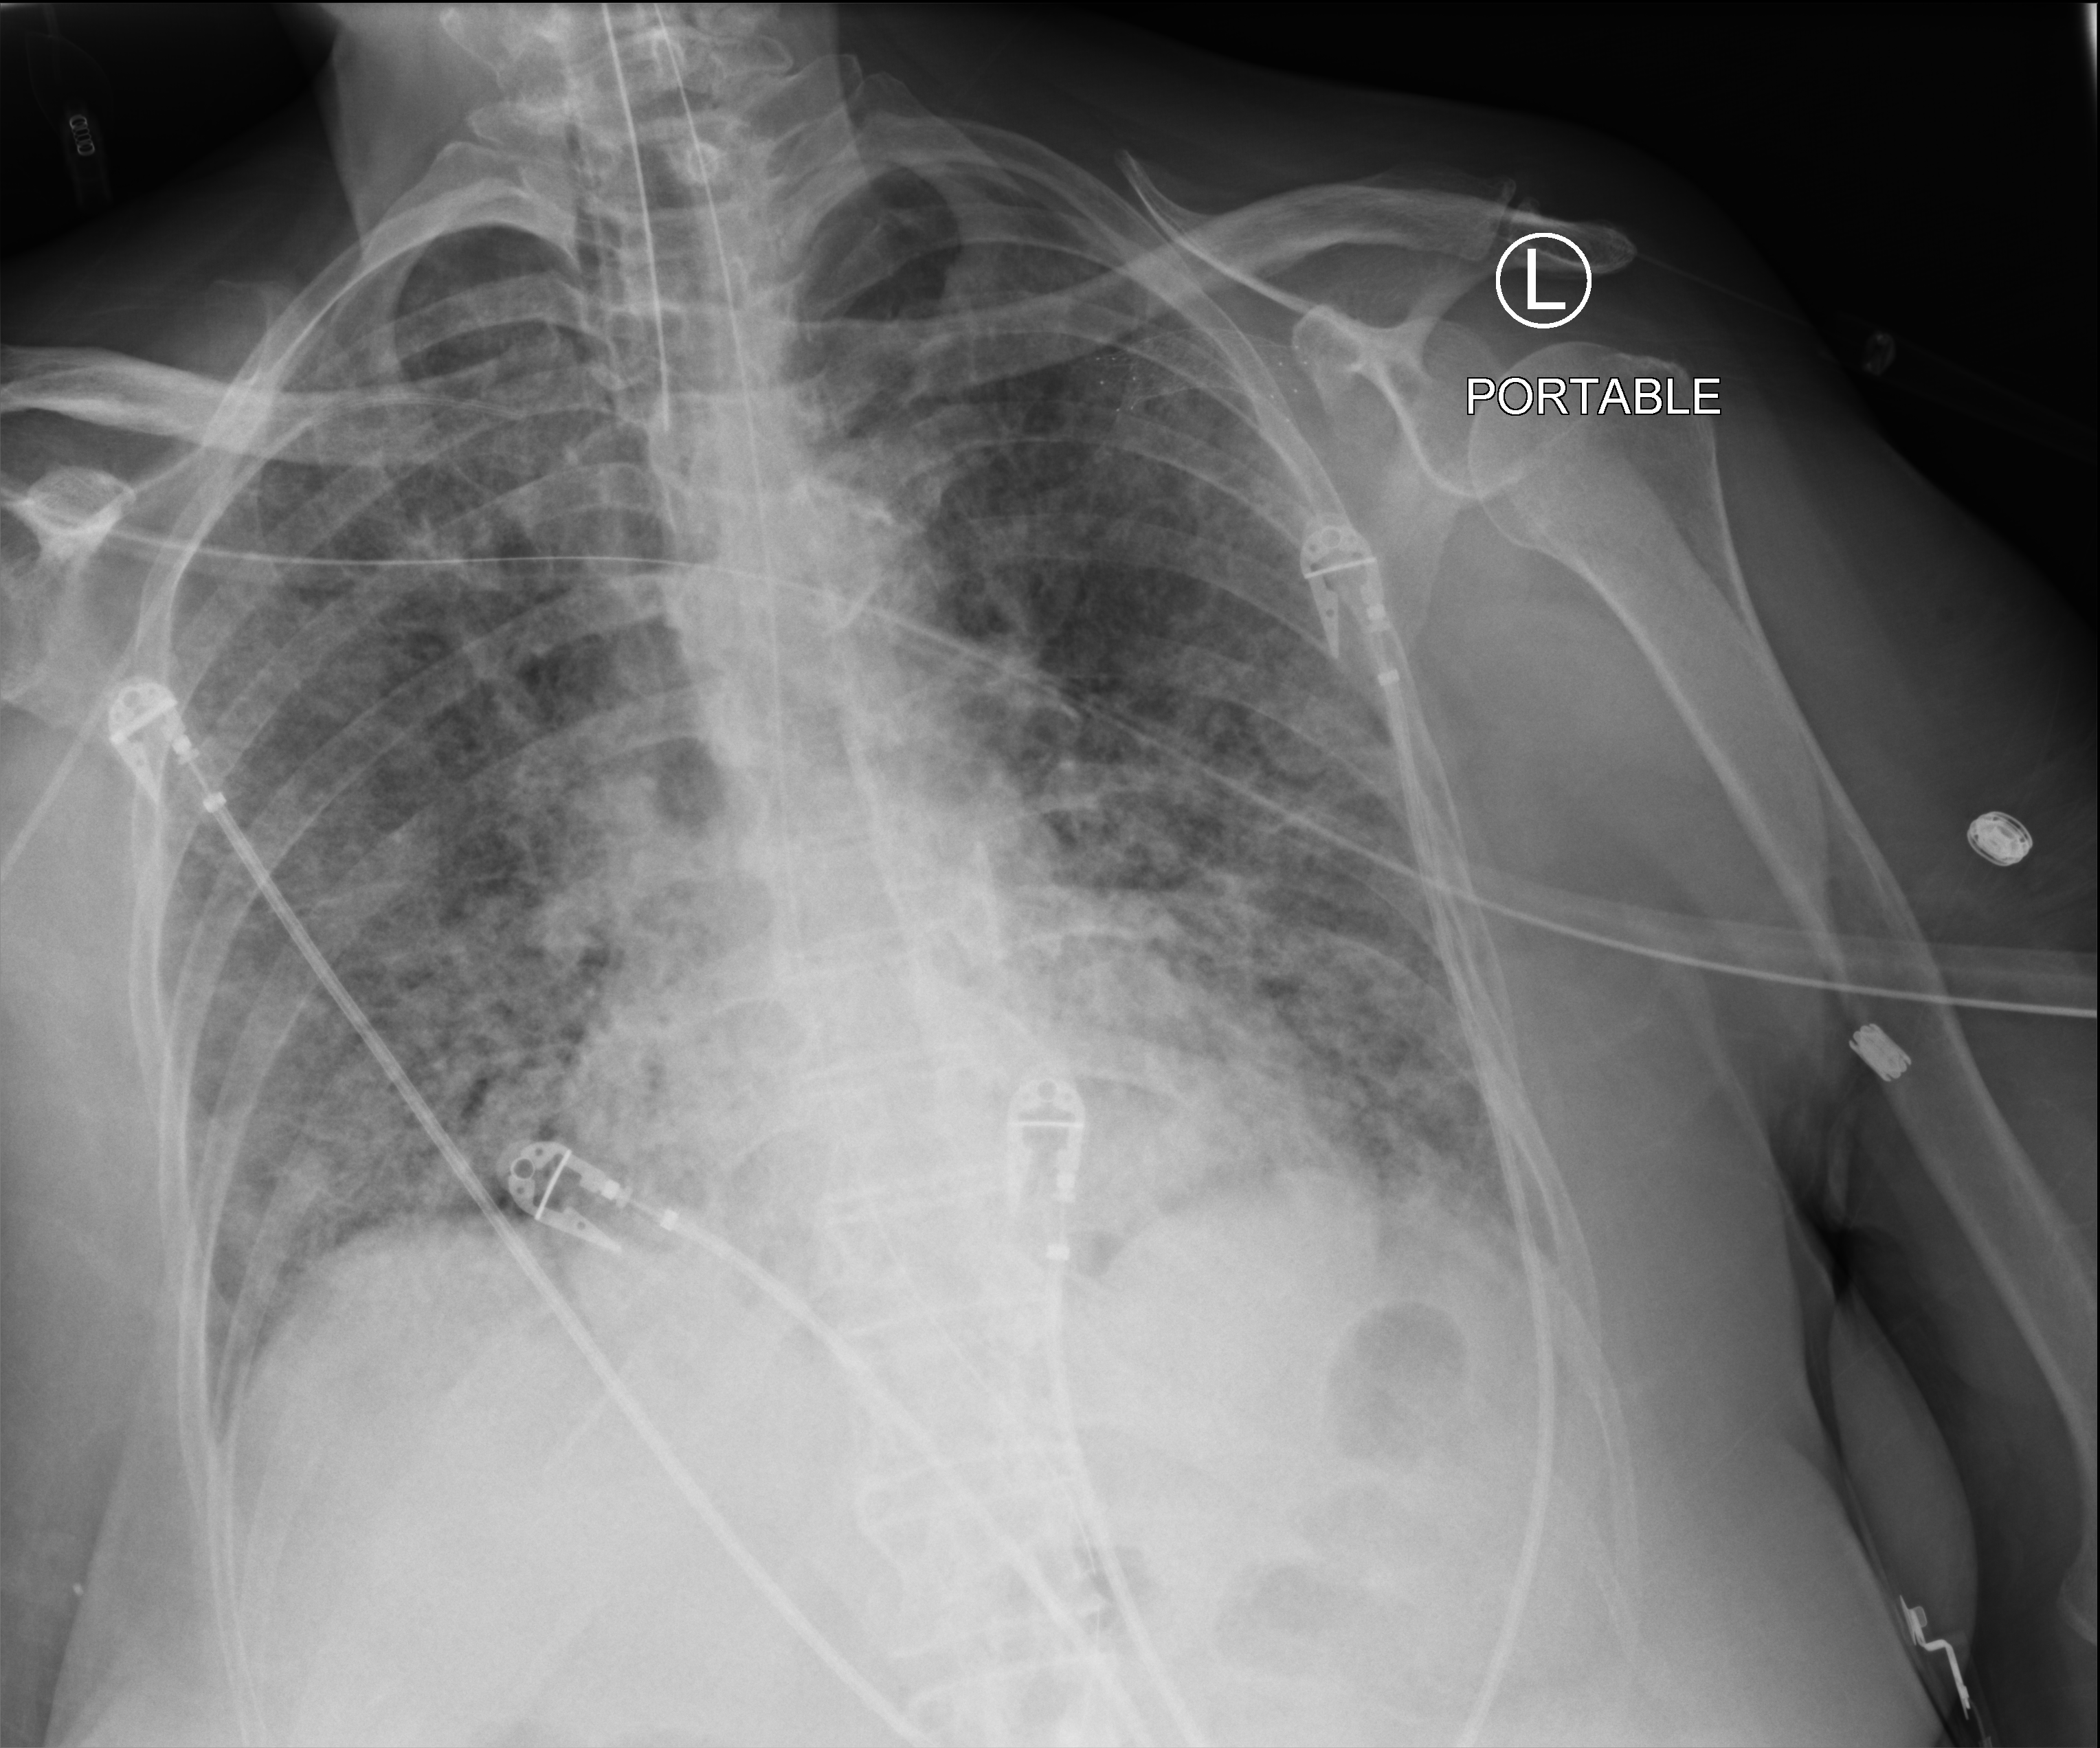
Bedside chest radiograph (computed radiography), anteroposterior (AP) projection. Female patient hospitalised with COVID-19, age 60–74 years.
Hospital-stay facts (about this admission, not read from this image; timing relative to this image not recorded): length of hospital stay: 23 days; diabetes (admission record): yes.